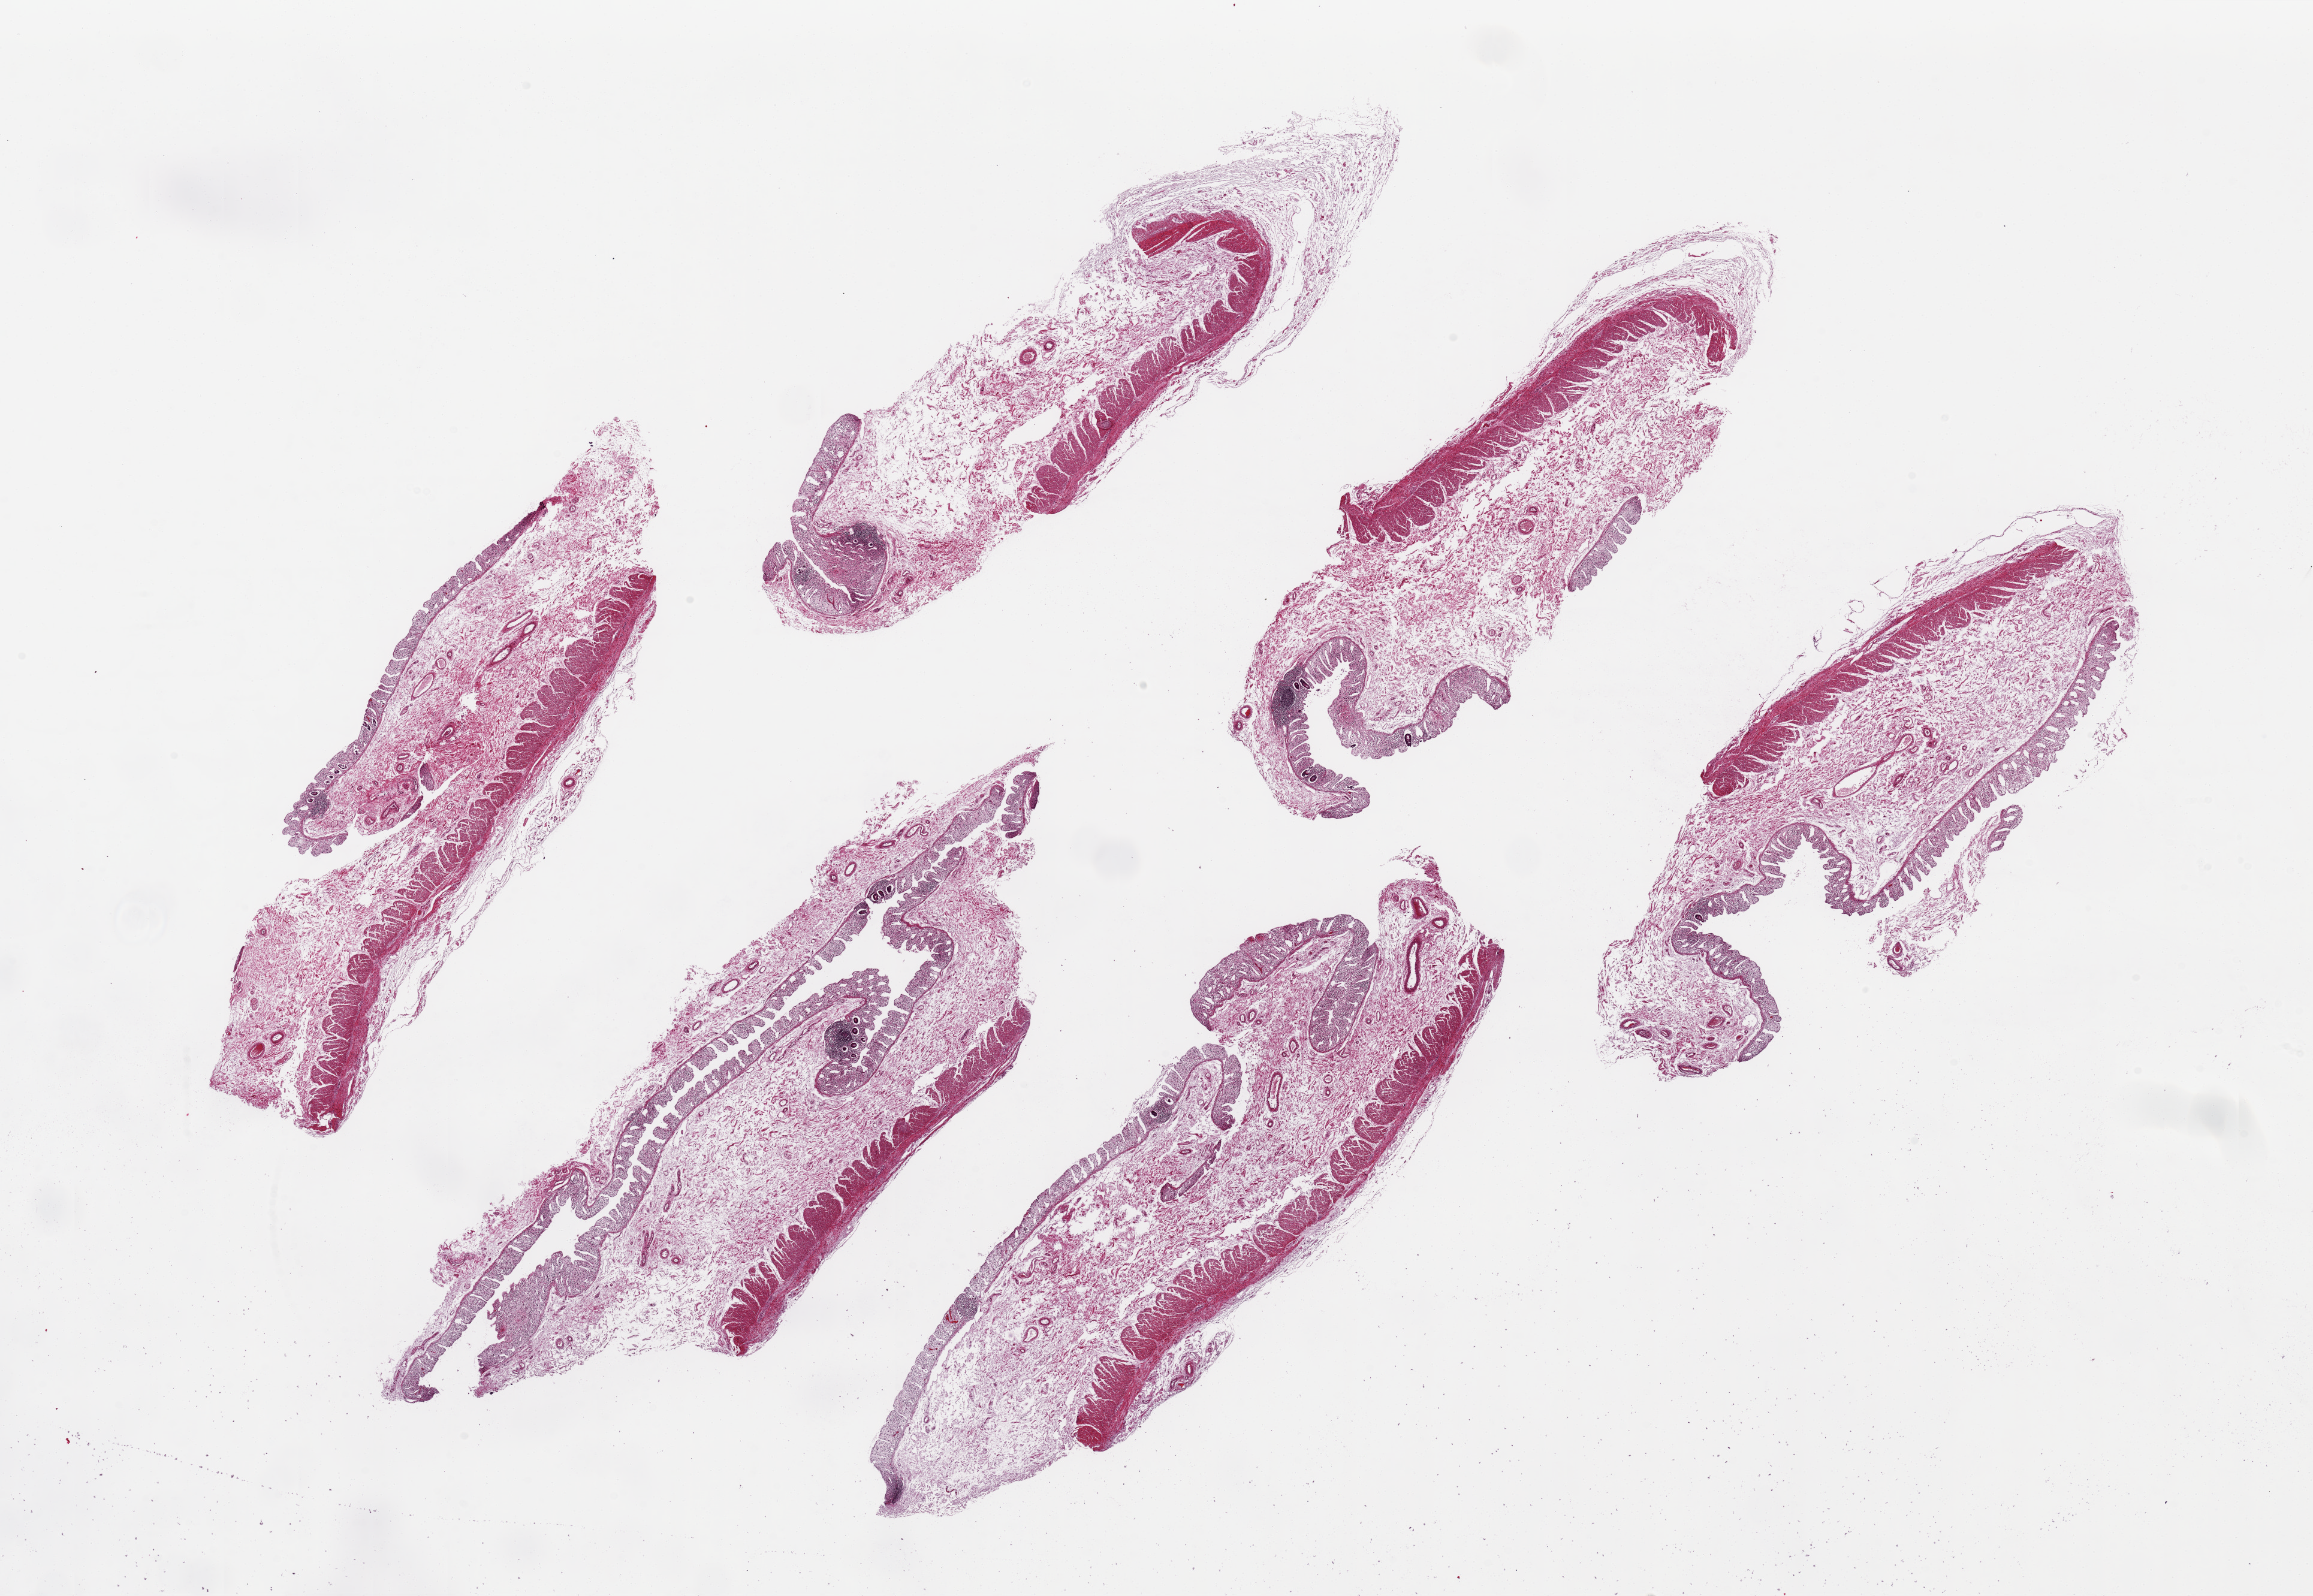
Whole-slide image, haematoxylin and eosin stain, low-resolution overview of the scanned area, about 30.5 x 21.1 mm; PAXgene-fixed, paraffin-embedded tissue; section of transverse colon (target tissue); tissue donor sample. Male donor.
* reviewer comment on this tissue sample: 6 pieces up to 12x3.5 mm; mucosa very autolyzed, muscle slightly autolyzed(1); lymphoid cells preserved; submucosa very edematous